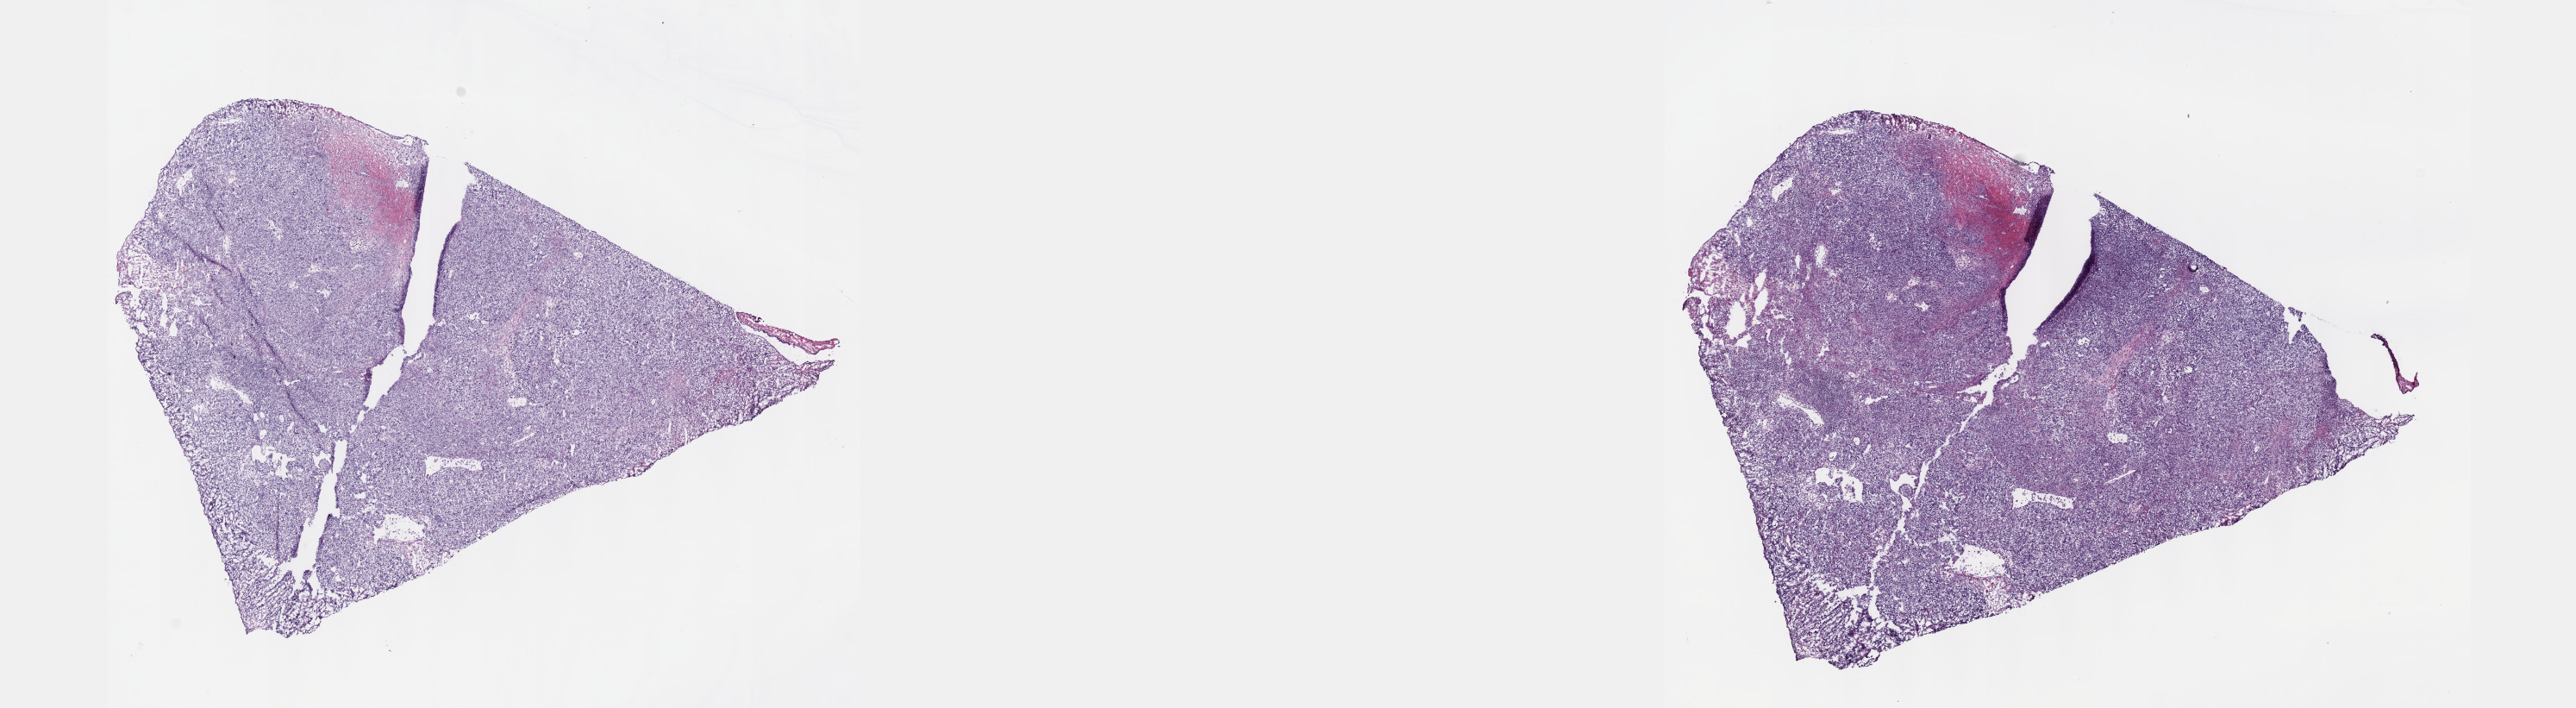
Digitized Hematoxylin and eosin (H&E) stained tissue section (whole slide) — whole scanned area (about 24.1 x 6.6 mm) shown as a low-resolution overview; frozen section from the top of the tissue portion; primary tumour sample from the testis. Male, age 30 years at initial diagnosis. Pathologist review of this section (percent, as recorded): tumour cells 100%, tumour nuclei 80%, normal cells 0%, stromal cells 0%, necrosis 0%. Infiltration values recorded for this section: lymphocyte infiltration 1%, monocyte infiltration 0%, neutrophil infiltration 0%.
* AJCC pathologic stage: IS
* diagnosis: Mixed germ cell tumor